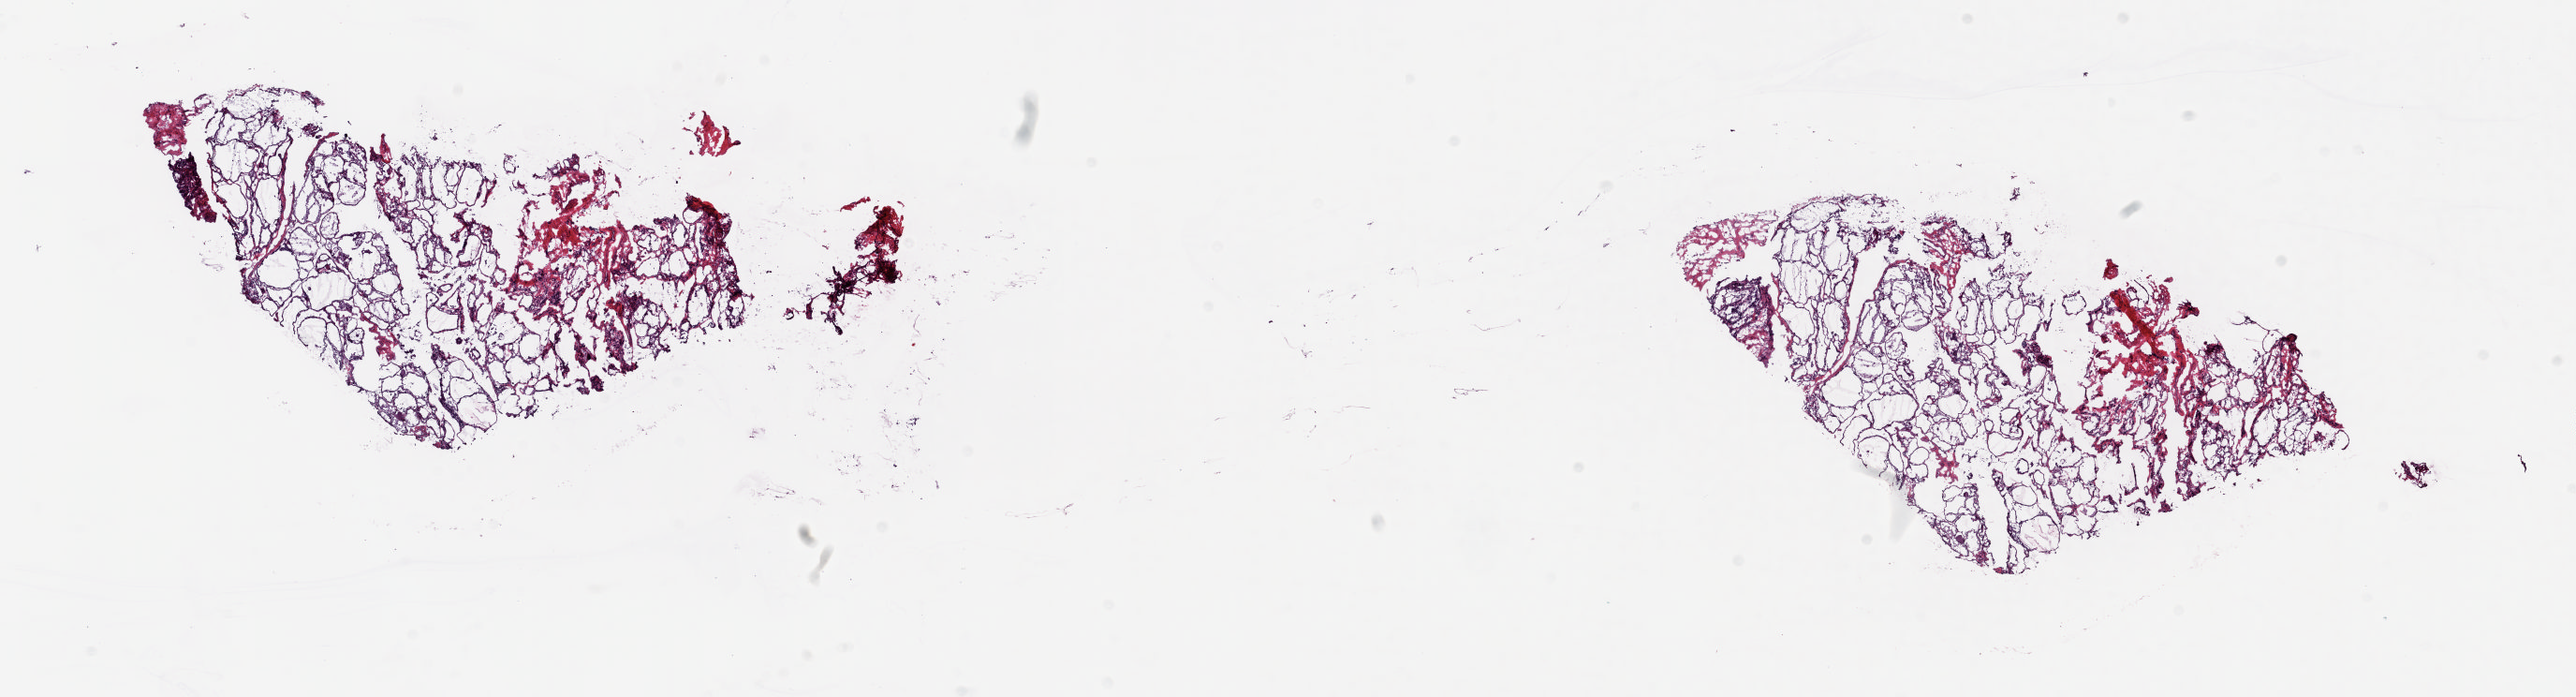
Whole-slide histology image, Hematoxylin and eosin (H&E) stained, shown as a low-resolution overview of the whole scanned area (about 21.8 x 5.9 mm, from a 20x scan), frozen section from the top of the tissue portion, thyroid, solid tissue normal (non-tumour tissue) sample. Female, age 36 years at initial diagnosis. Slide review estimates, as recorded: tumour cells 0%, tumour nuclei 0%.
This section: solid tissue normal (non-tumour) sample from the same patient. Patient diagnosis: Papillary adenocarcinoma, NOS (thyroid gland).